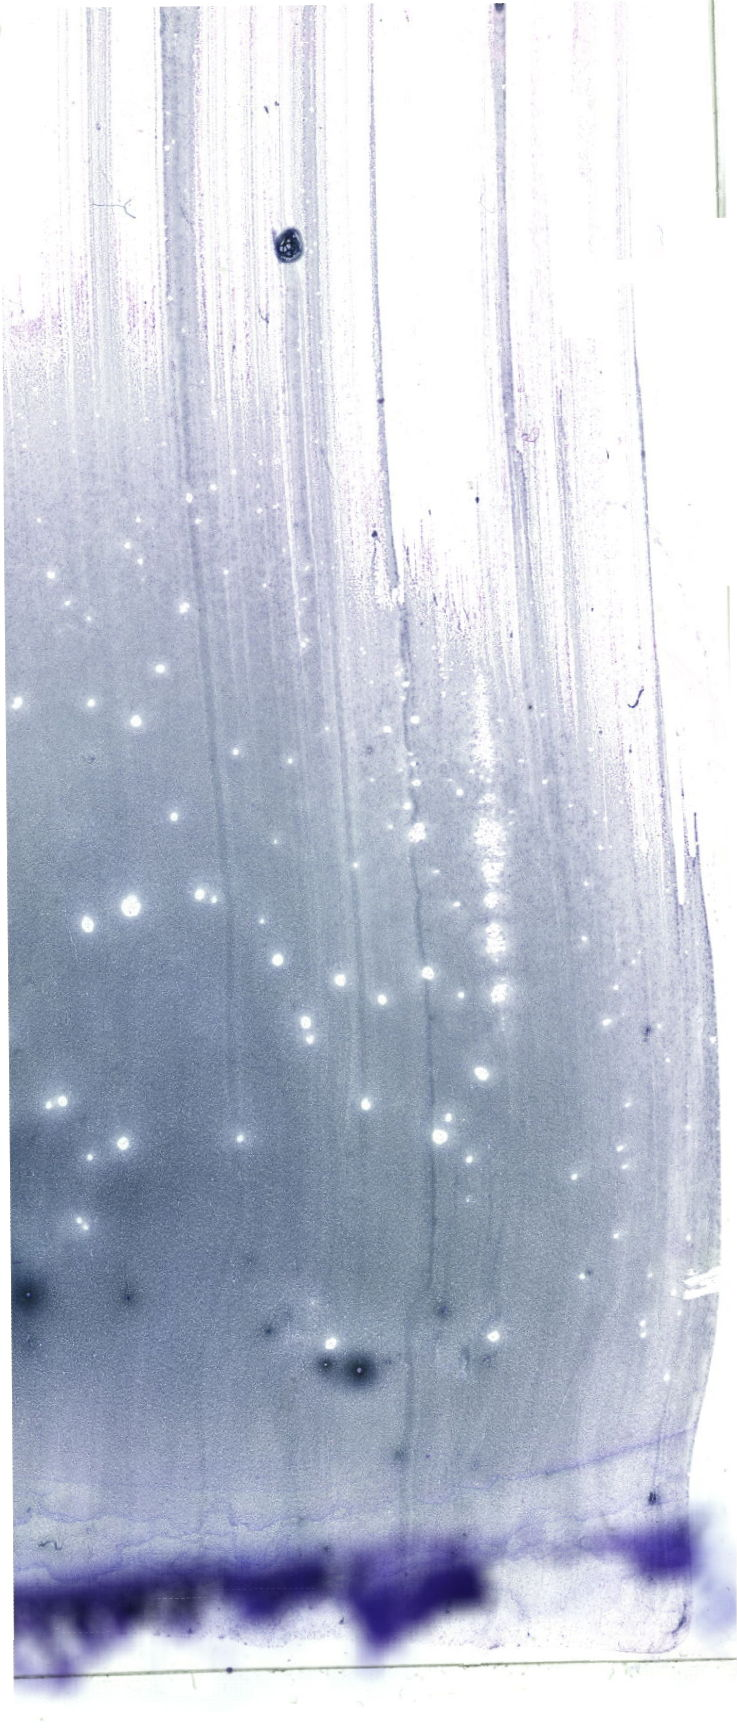
Bone marrow aspirate smear, May-Grünwald-Giemsa (MGG) stain, whole-slide image, whole scanned area (about 20.9 x 49.2 mm) shown as a low-resolution overview. Patient sex: male.
• diagnosis: B Acute Lymphoblastic Leukemia